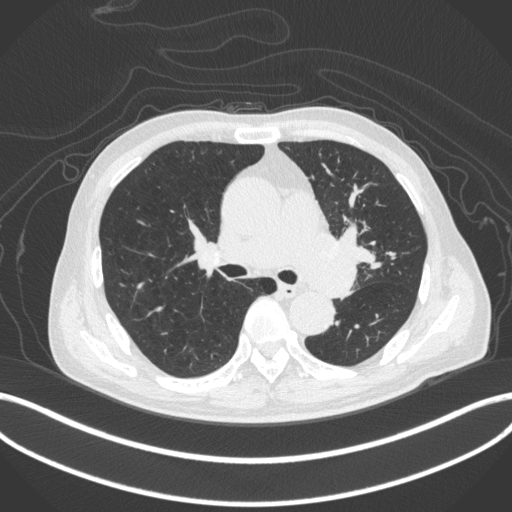
Chest CT, one axial slice. Slice 264 of 420 in the series (ordered by position). Lung window (W 1500 / L -600 HU). 1 mm slice thickness. 512 × 512 image matrix, field of view 400 × 400 mm. Patient: male, 77 years. From the clinical record (not read from this slice): clinical TNM (as recorded): T3 N1 M0.
Structures marked on this image (rectangle marked by the reading radiologist):
- lung tumour (recorded histology: adenocarcinoma): box from (x=291, y=224) to (x=370, y=302) px